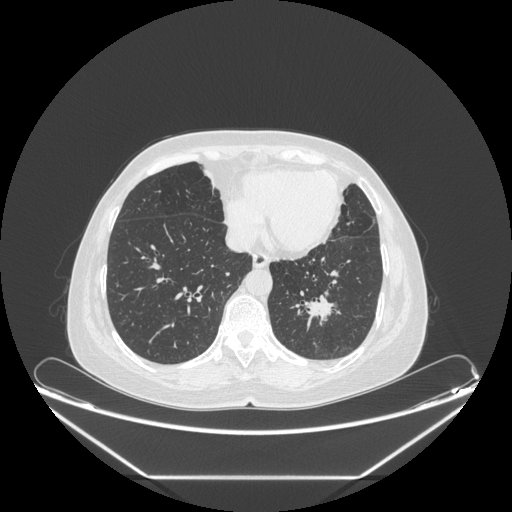
Chest CT, one axial slice. Position 79 of 241 along the scan axis. Reconstruction kernel STANDARD. Lung window (W 1500 / L -600 HU). 1.25 mm slice thickness. 512 × 512 image matrix, field of view 451 × 451 mm. Patient: female, 63 years. Case-level facts recorded for this patient, not image findings: clinical TNM (as recorded): T1c N0 M0; histopathological grade: G2-3.
Outlined on this slice (bounding box drawn by a radiologist):
- lung tumour (recorded histology: adenocarcinoma): bounding box (x1, y1, x2, y2) in pixels: (294, 289, 337, 335)